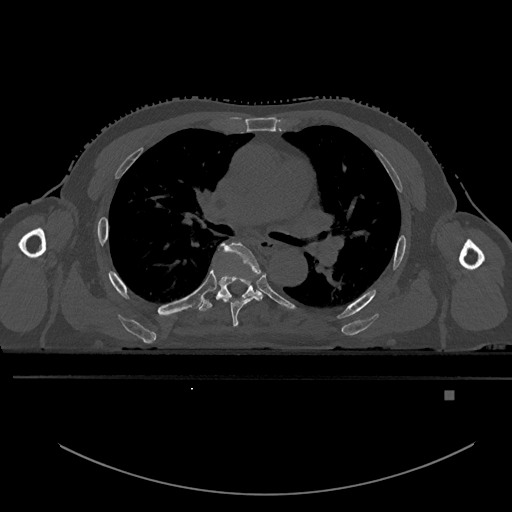
CT including the spine, one axial slice; position 334 of 969 along the scan axis; bone window (W 1800 / L 400 HU); 512 × 512 image matrix. Male patient, age 82 years. From the clinical record (not read from this slice): primary cancer: prostate; vertebrae with lytic lesions (as recorded): T11, T9, T8, T2.
Annotated regions visible in this slice (semi-automatic segmentation, software-assisted and operator-edited):
- T5 vertebra: box from (x=220, y=242) to (x=262, y=328) px
- T6 vertebra: (x=196, y=245)–(x=261, y=312)